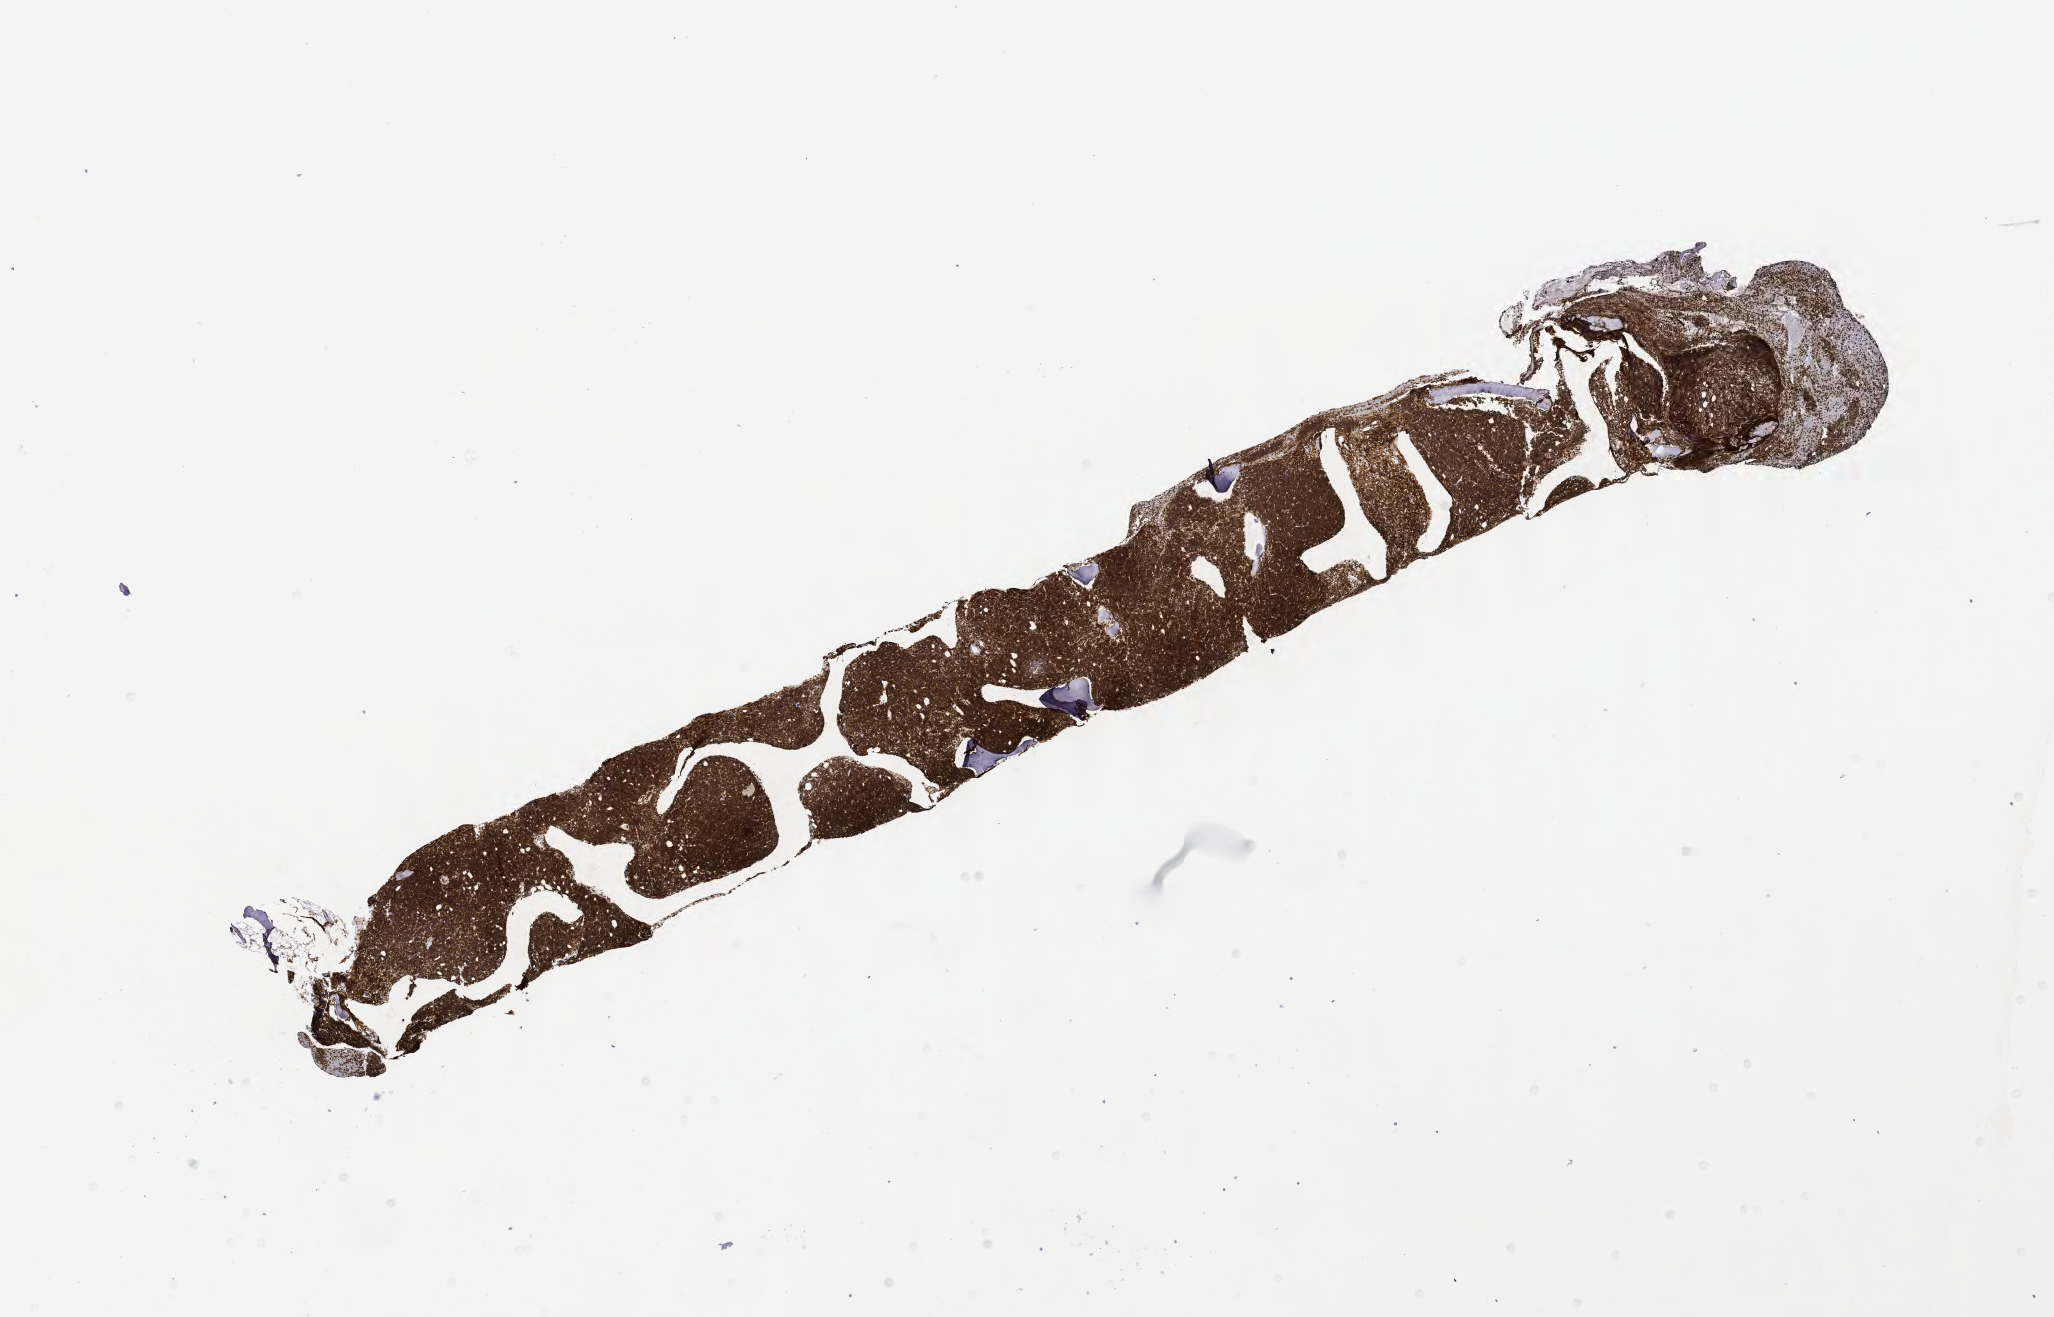
IHC for CD20, whole-slide image — shown as a low-resolution overview of the whole scanned area (about 16.6 x 10.6 mm). Specimen: tumor tissue. Patient: female, age 64 years.
- histologic diagnosis: Burkitt lymphoma, NOS